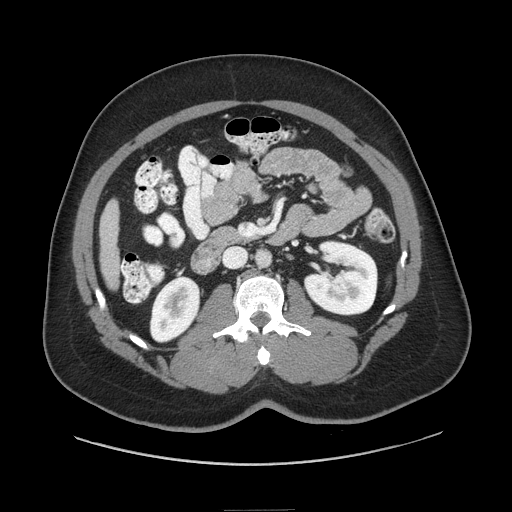
Contrast-enhanced abdominal CT (liver protocol), one axial slice. Slice 18 of 87 in the series (ordered by position). Reconstruction kernel STANDARD. Soft-tissue window (W 400 / L 40 HU). 2.5 mm slice thickness. 512 × 512 image matrix, field of view 440 × 440 mm. Case-level facts recorded for this patient, not image findings: diagnosis: hepatocellular carcinoma (patient treated with transarterial chemoembolisation; whether this scan precedes or follows treatment is not stated here); TNM stage (as recorded): Stage-II; Child-Pugh class: A; tumour nodularity: uninodular.
Structures marked on this image (semi-automatic segmentation, software-assisted and operator-edited):
- liver parenchyma outside the tumour (the mass and vessels are separate outlines, so this box may not span the whole liver): bounding box <99,200,118,288> (left, top, right, bottom; pixels)